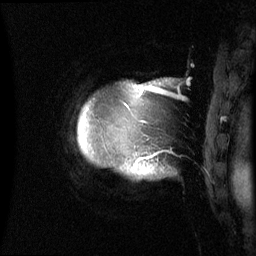
Breast MRI (dynamic contrast-enhanced), one sagittal slice; slice 58 of 60 in the series (ordered by position); dynamic contrast-enhanced series, image 2 of 3 at this slice position (ordered by acquisition); 1.5 T; TE 4.2 ms, TR 8.4 ms; 256 × 256 image matrix, field of view 230 × 230 mm. Patient: female, 48 years.
Structures marked on this image (semi-automatically segmented with operator editing):
- analysis volume of interest (the breast-tissue region the enhancement analysis was run in; not a lesion): bounding box (x1, y1, x2, y2) in pixels: (78, 83, 162, 176)
- tumour enhancement mask (voxels above the 70 % enhancement threshold inside the analysis volume of interest): (138, 86, 152, 160)